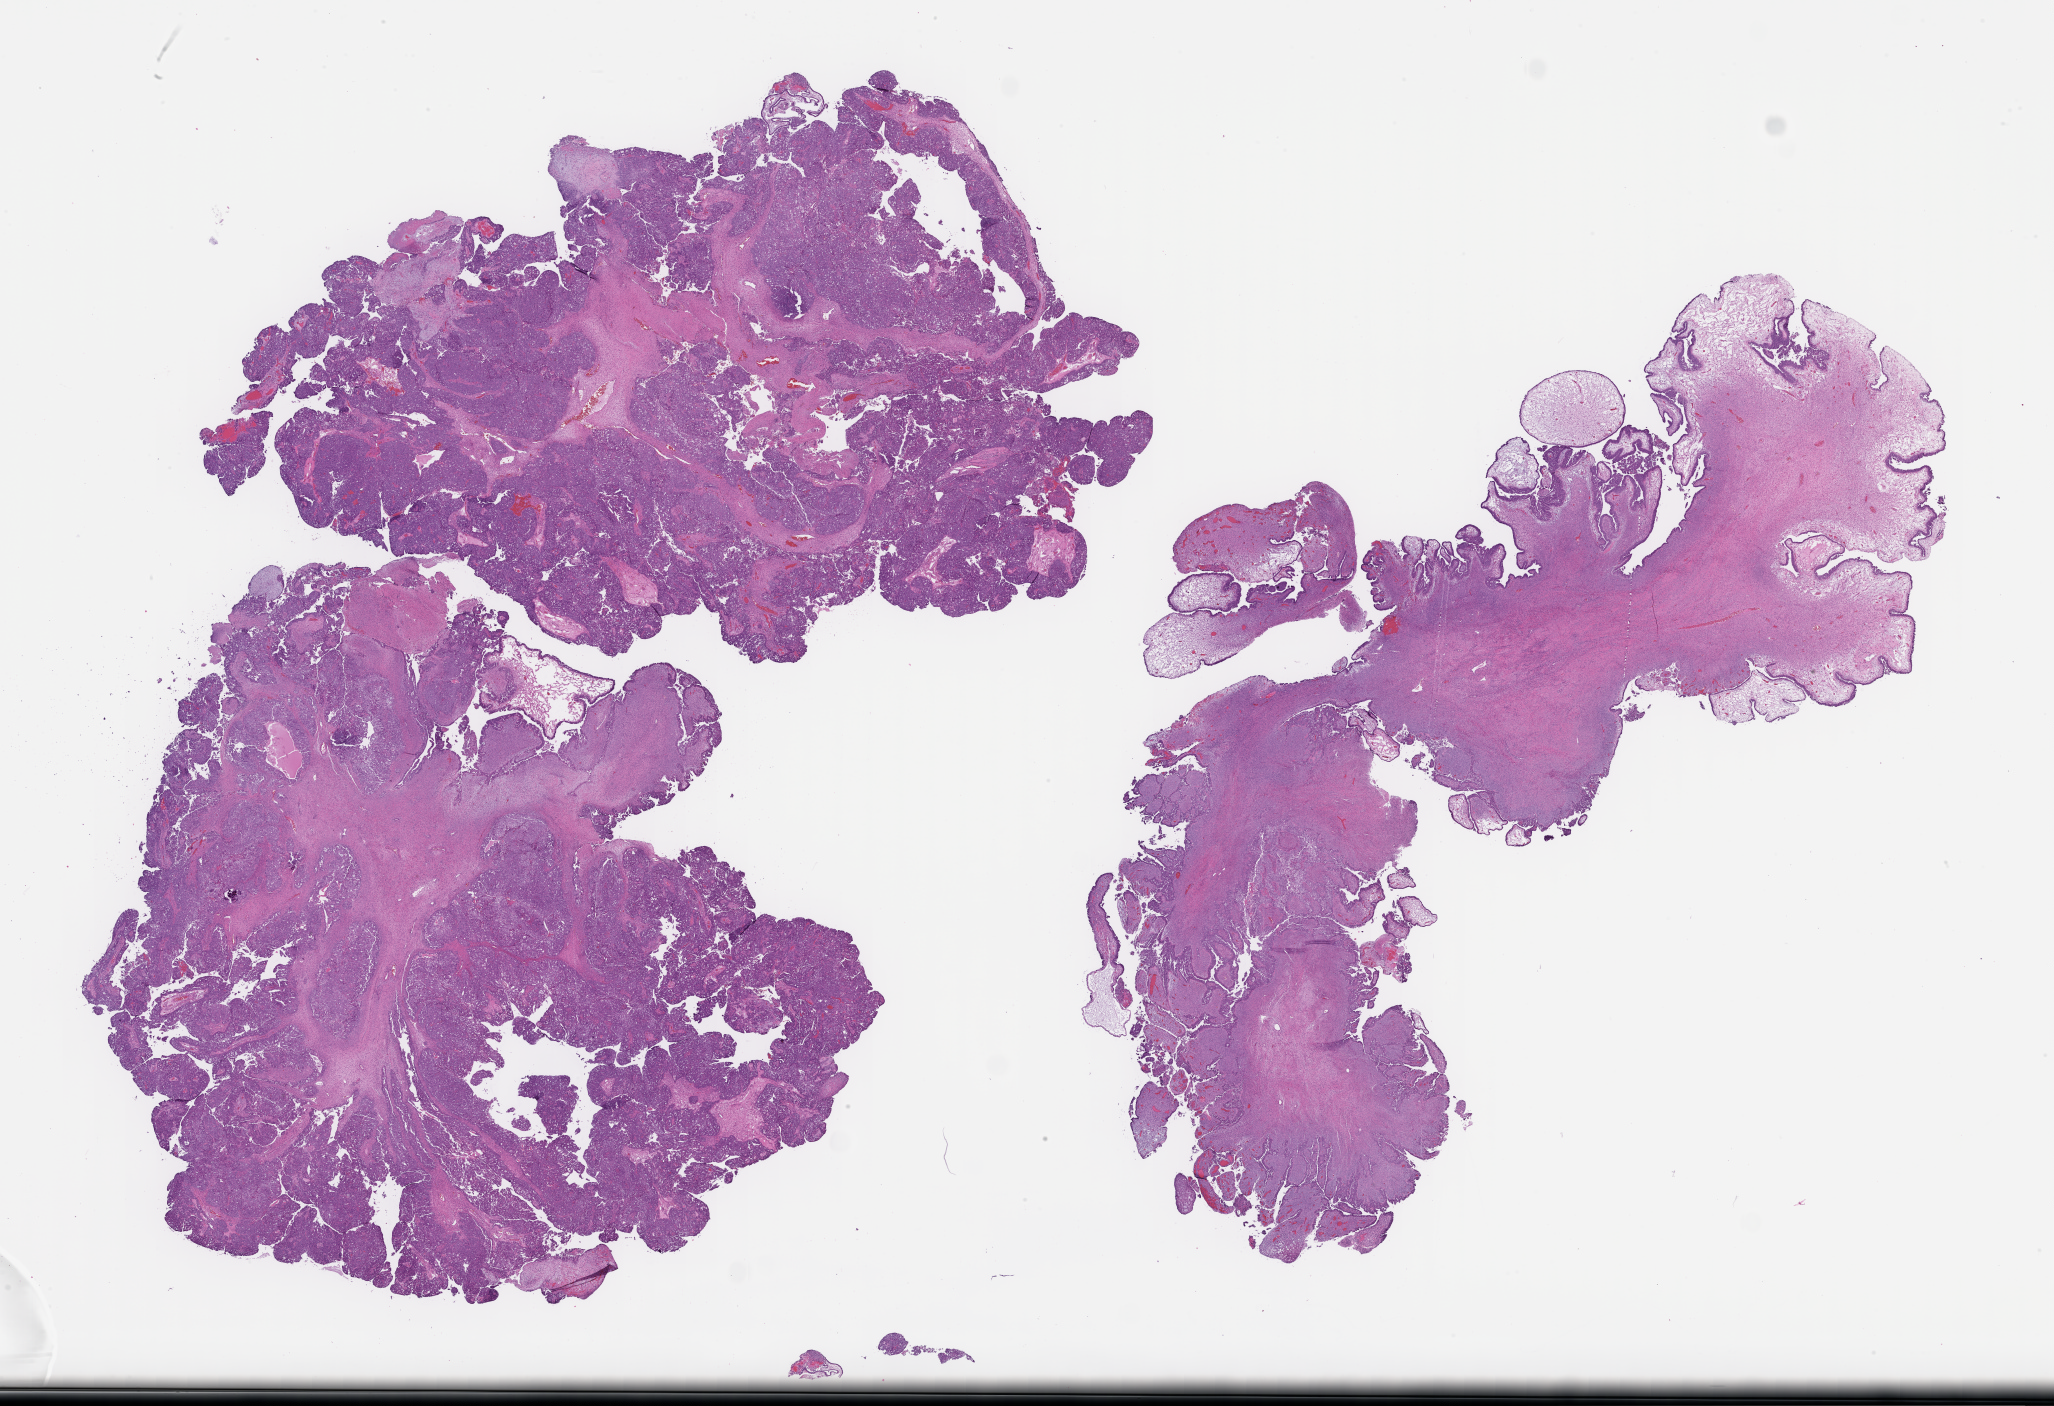
Hematoxylin and eosin (H&E) whole-slide image — low-resolution overview of the scanned area, about 33.2 x 22.7 mm; formalin-fixed paraffin-embedded section; site: ovary; specimen time point: archival tissue. Patient sex: female.
Patient diagnosis: Ovarian Carcinoma.